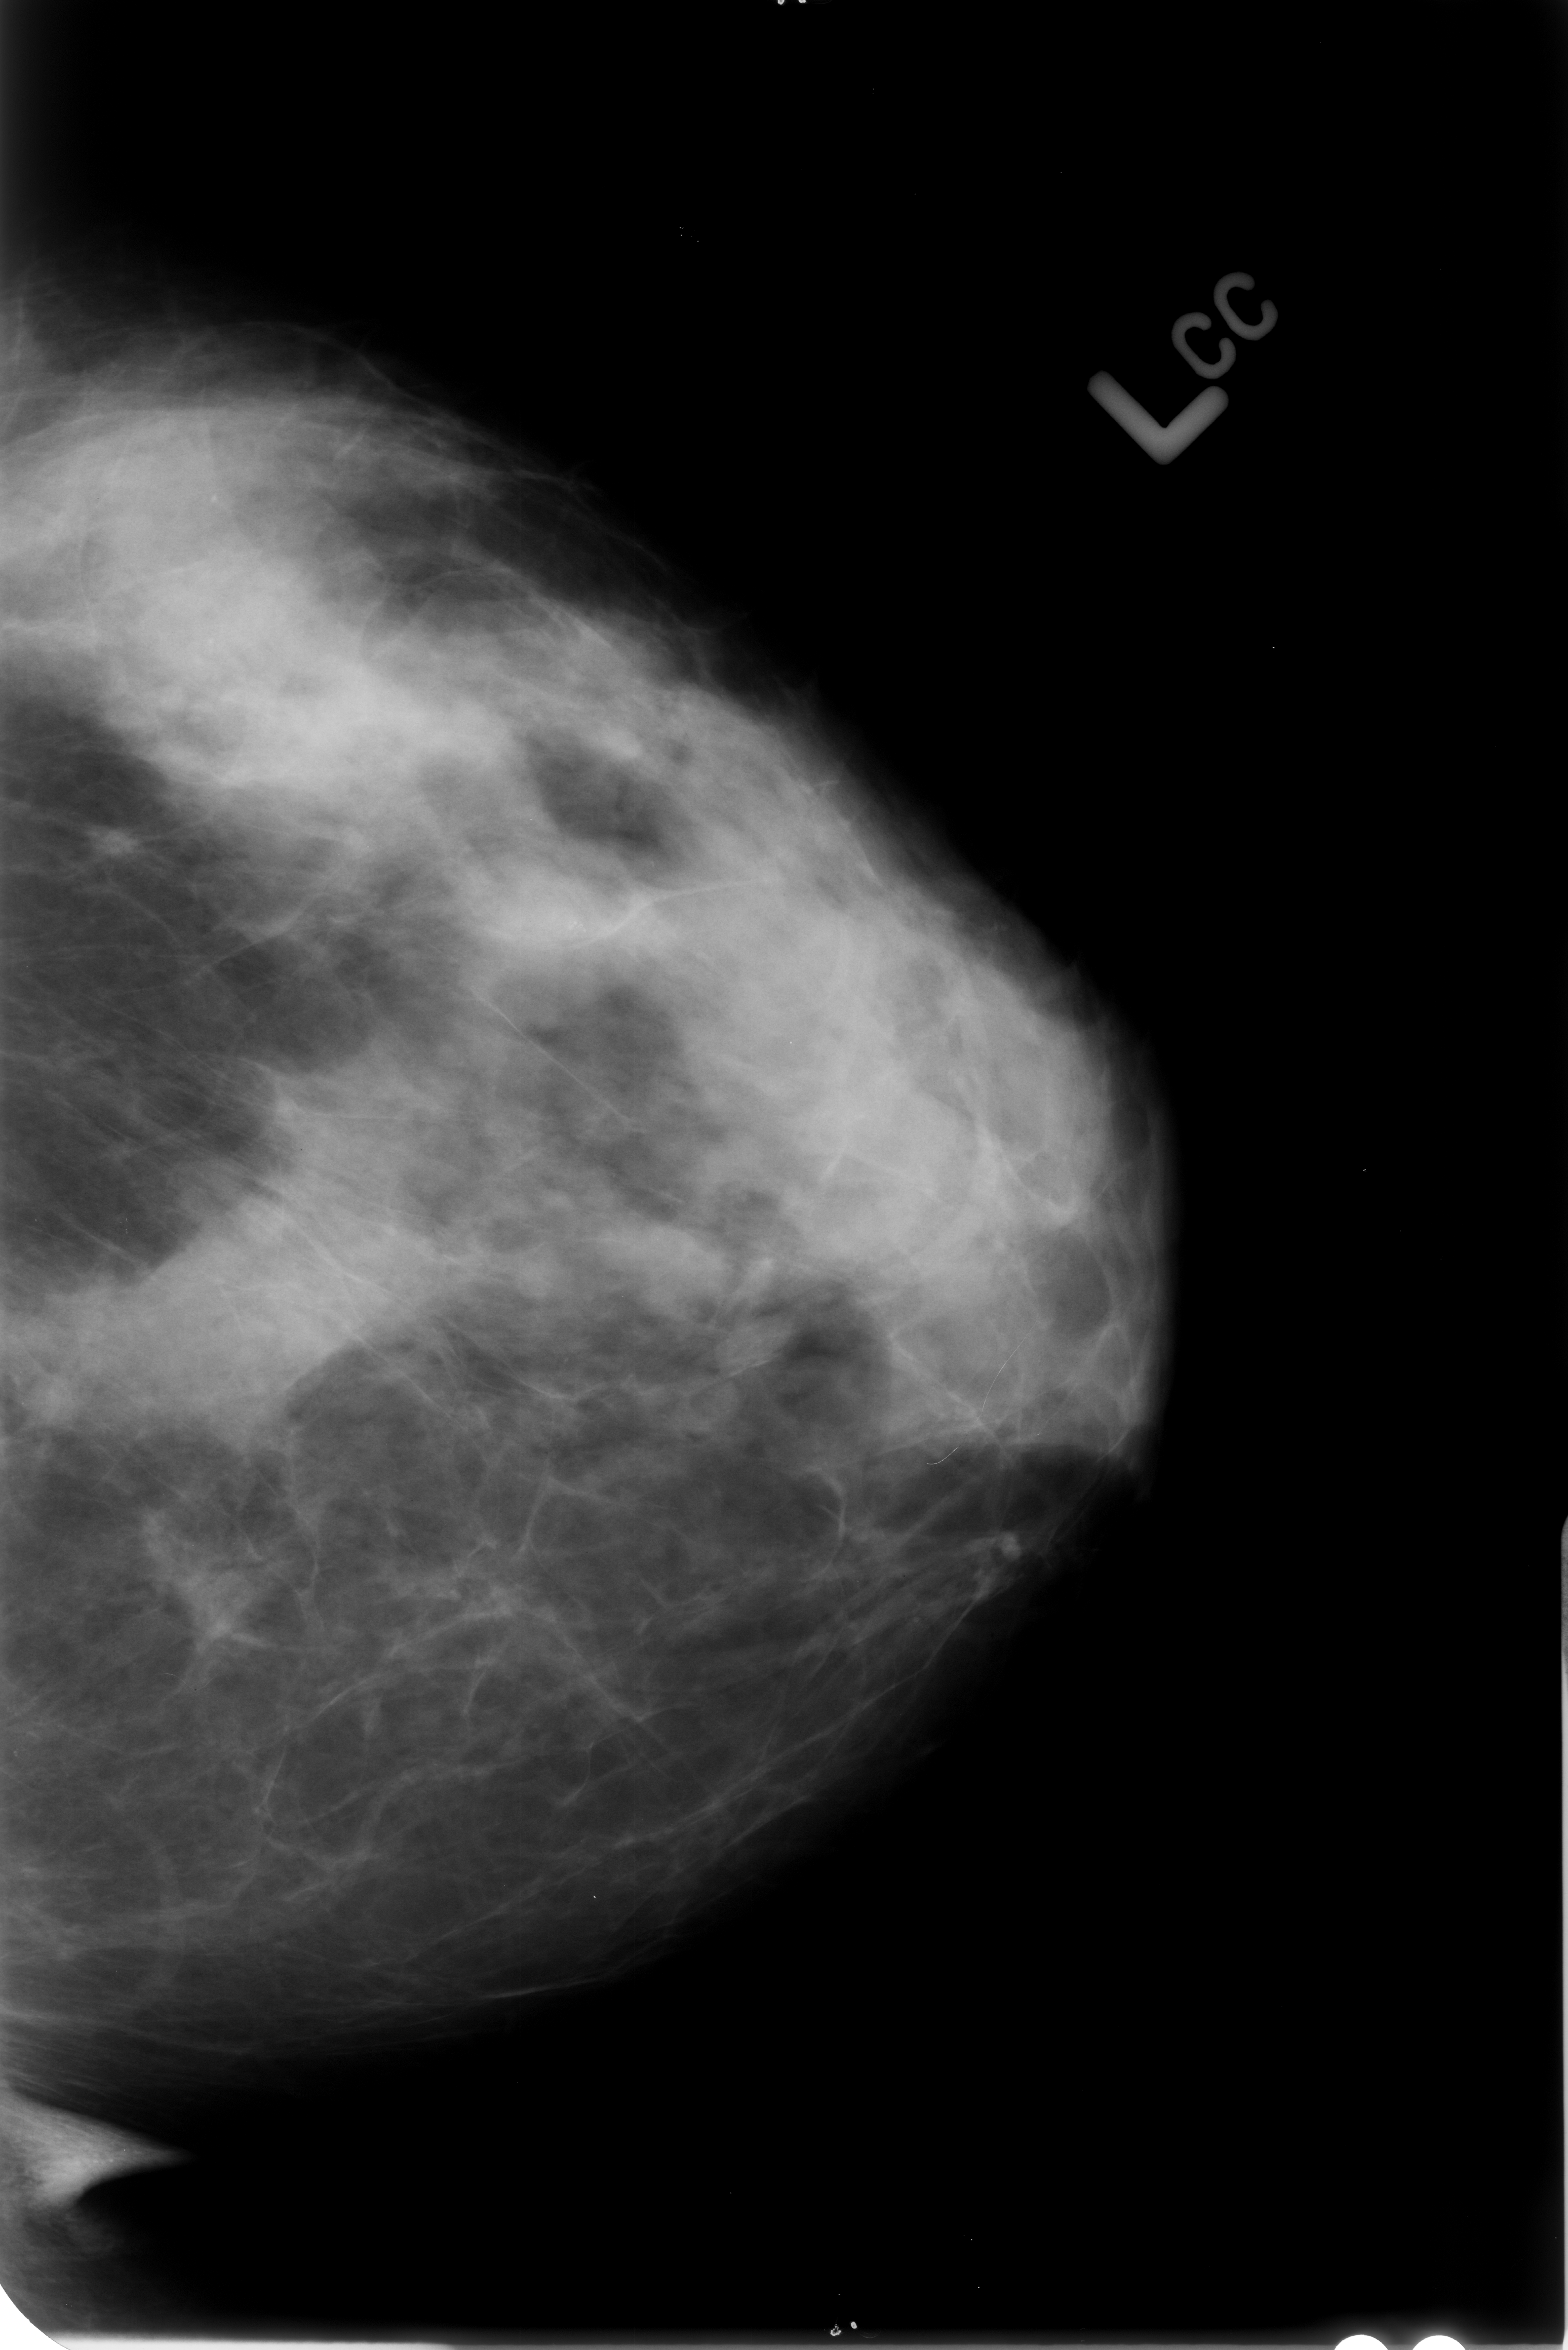
Digitized screen-film mammogram, left breast, CC view, BI-RADS breast density category 3 (scale 1–4).
Calcifications, morphology pleomorphic, distribution clustered; BI-RADS assessment category 4; subtlety rating 3 on a 1 (subtle) to 5 (obvious) scale; pathology result (as recorded, not read from the image): benign.